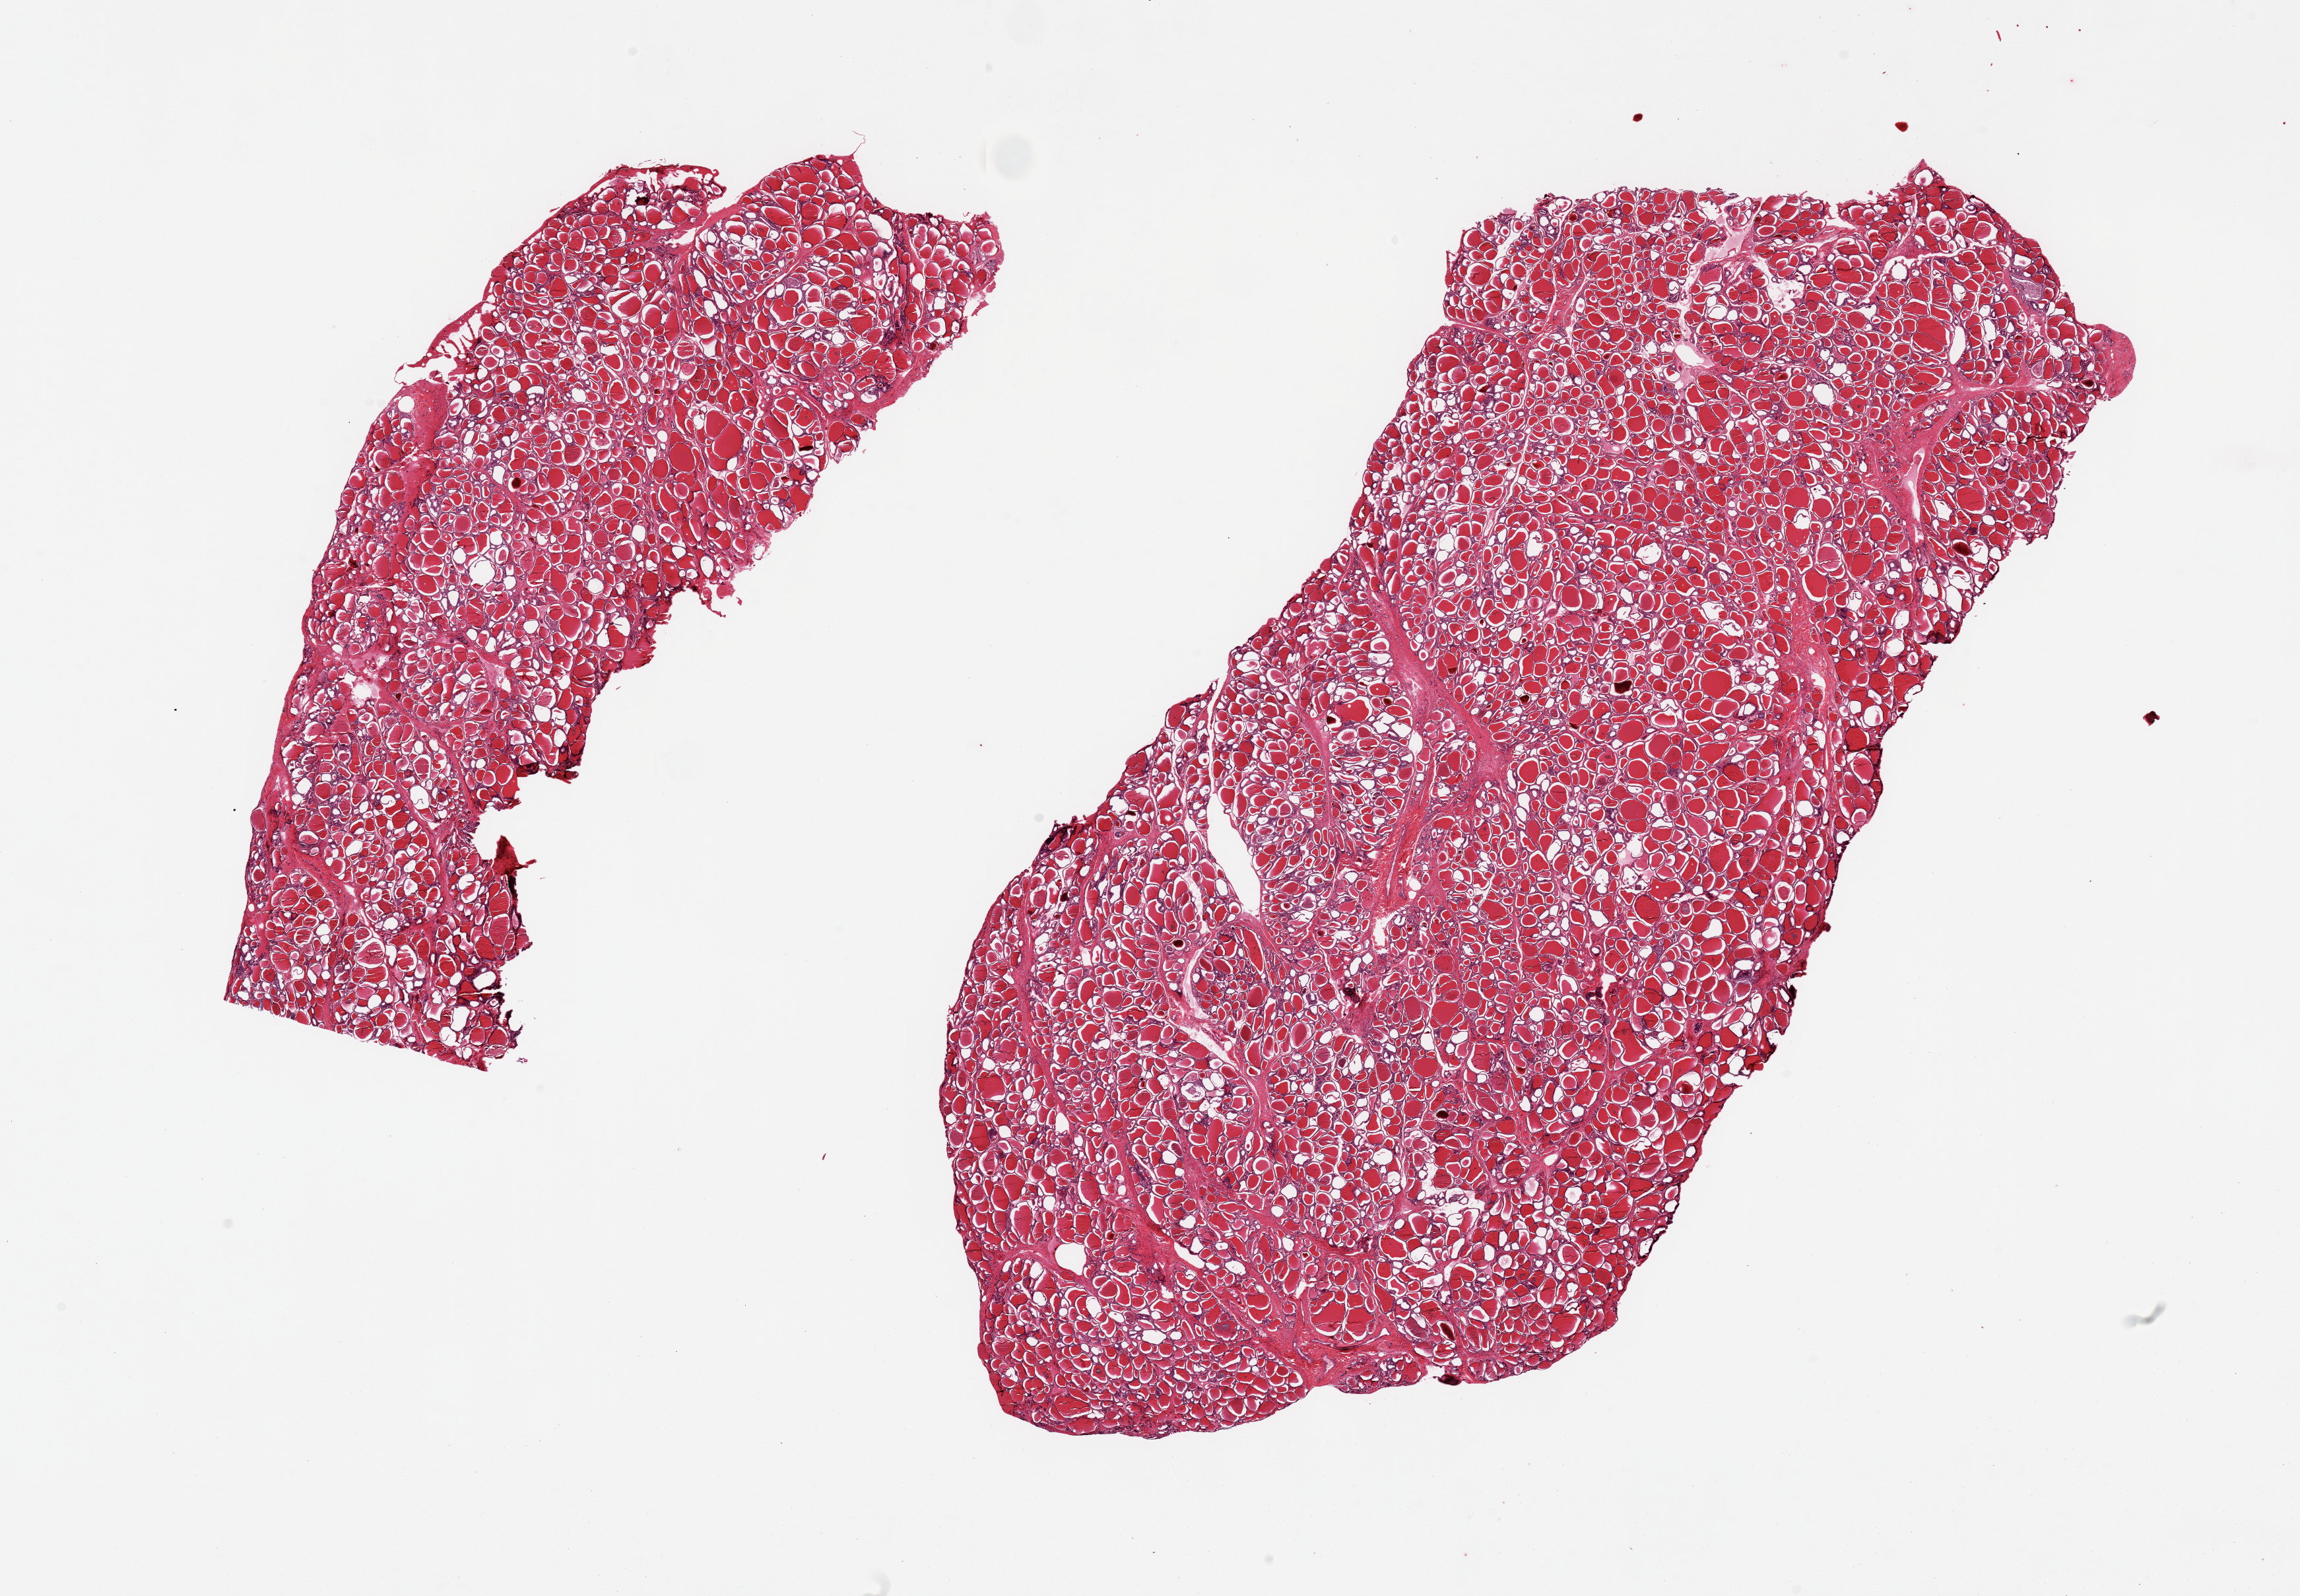
Hematoxylin and eosin (H&E) whole-slide image, brightfield, shown as a low-resolution overview of the whole scanned area (about 27.6 x 19.1 mm), PAXgene-fixed, paraffin-embedded tissue, target tissue: thyroid, donor tissue sample.
Pathologist's review note for this sample: 2 pieces.